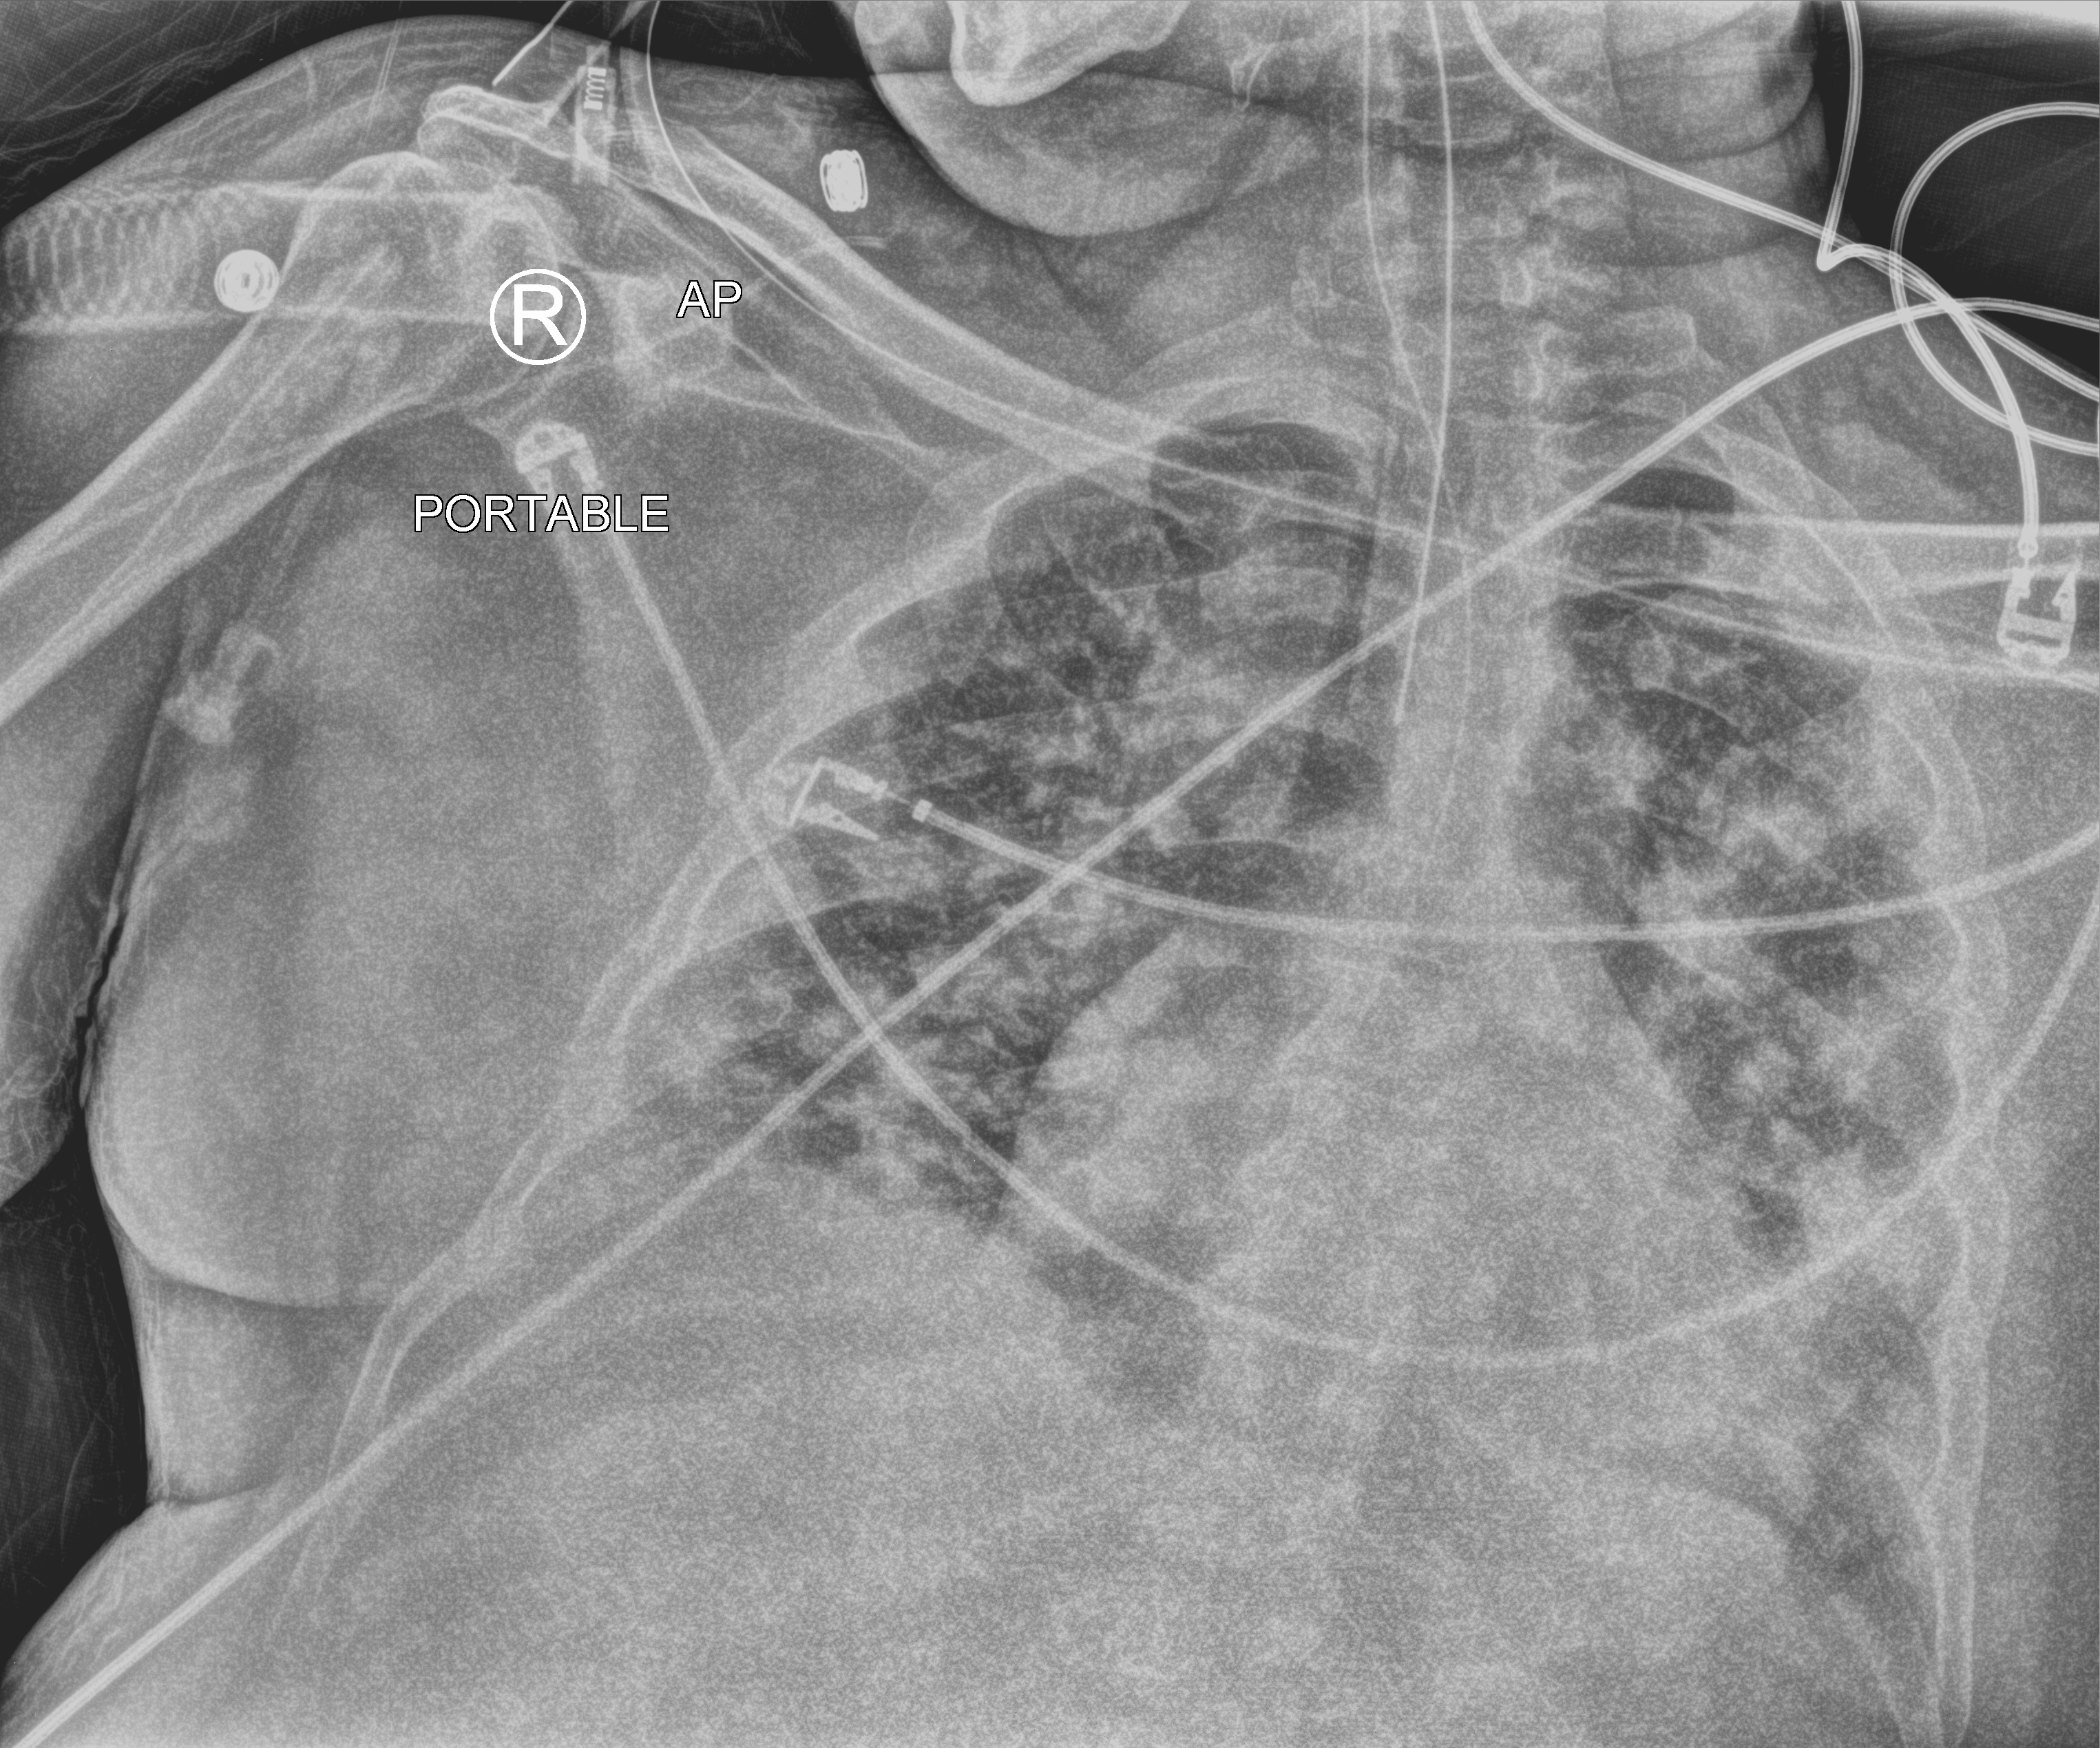
Bedside chest radiograph (computed radiography); anteroposterior (AP) projection. Male patient hospitalised with COVID-19, age 18–59 years.
Hospital-stay facts (about this admission, not read from this image; timing relative to this image not recorded): chronic kidney disease (admission record): no.